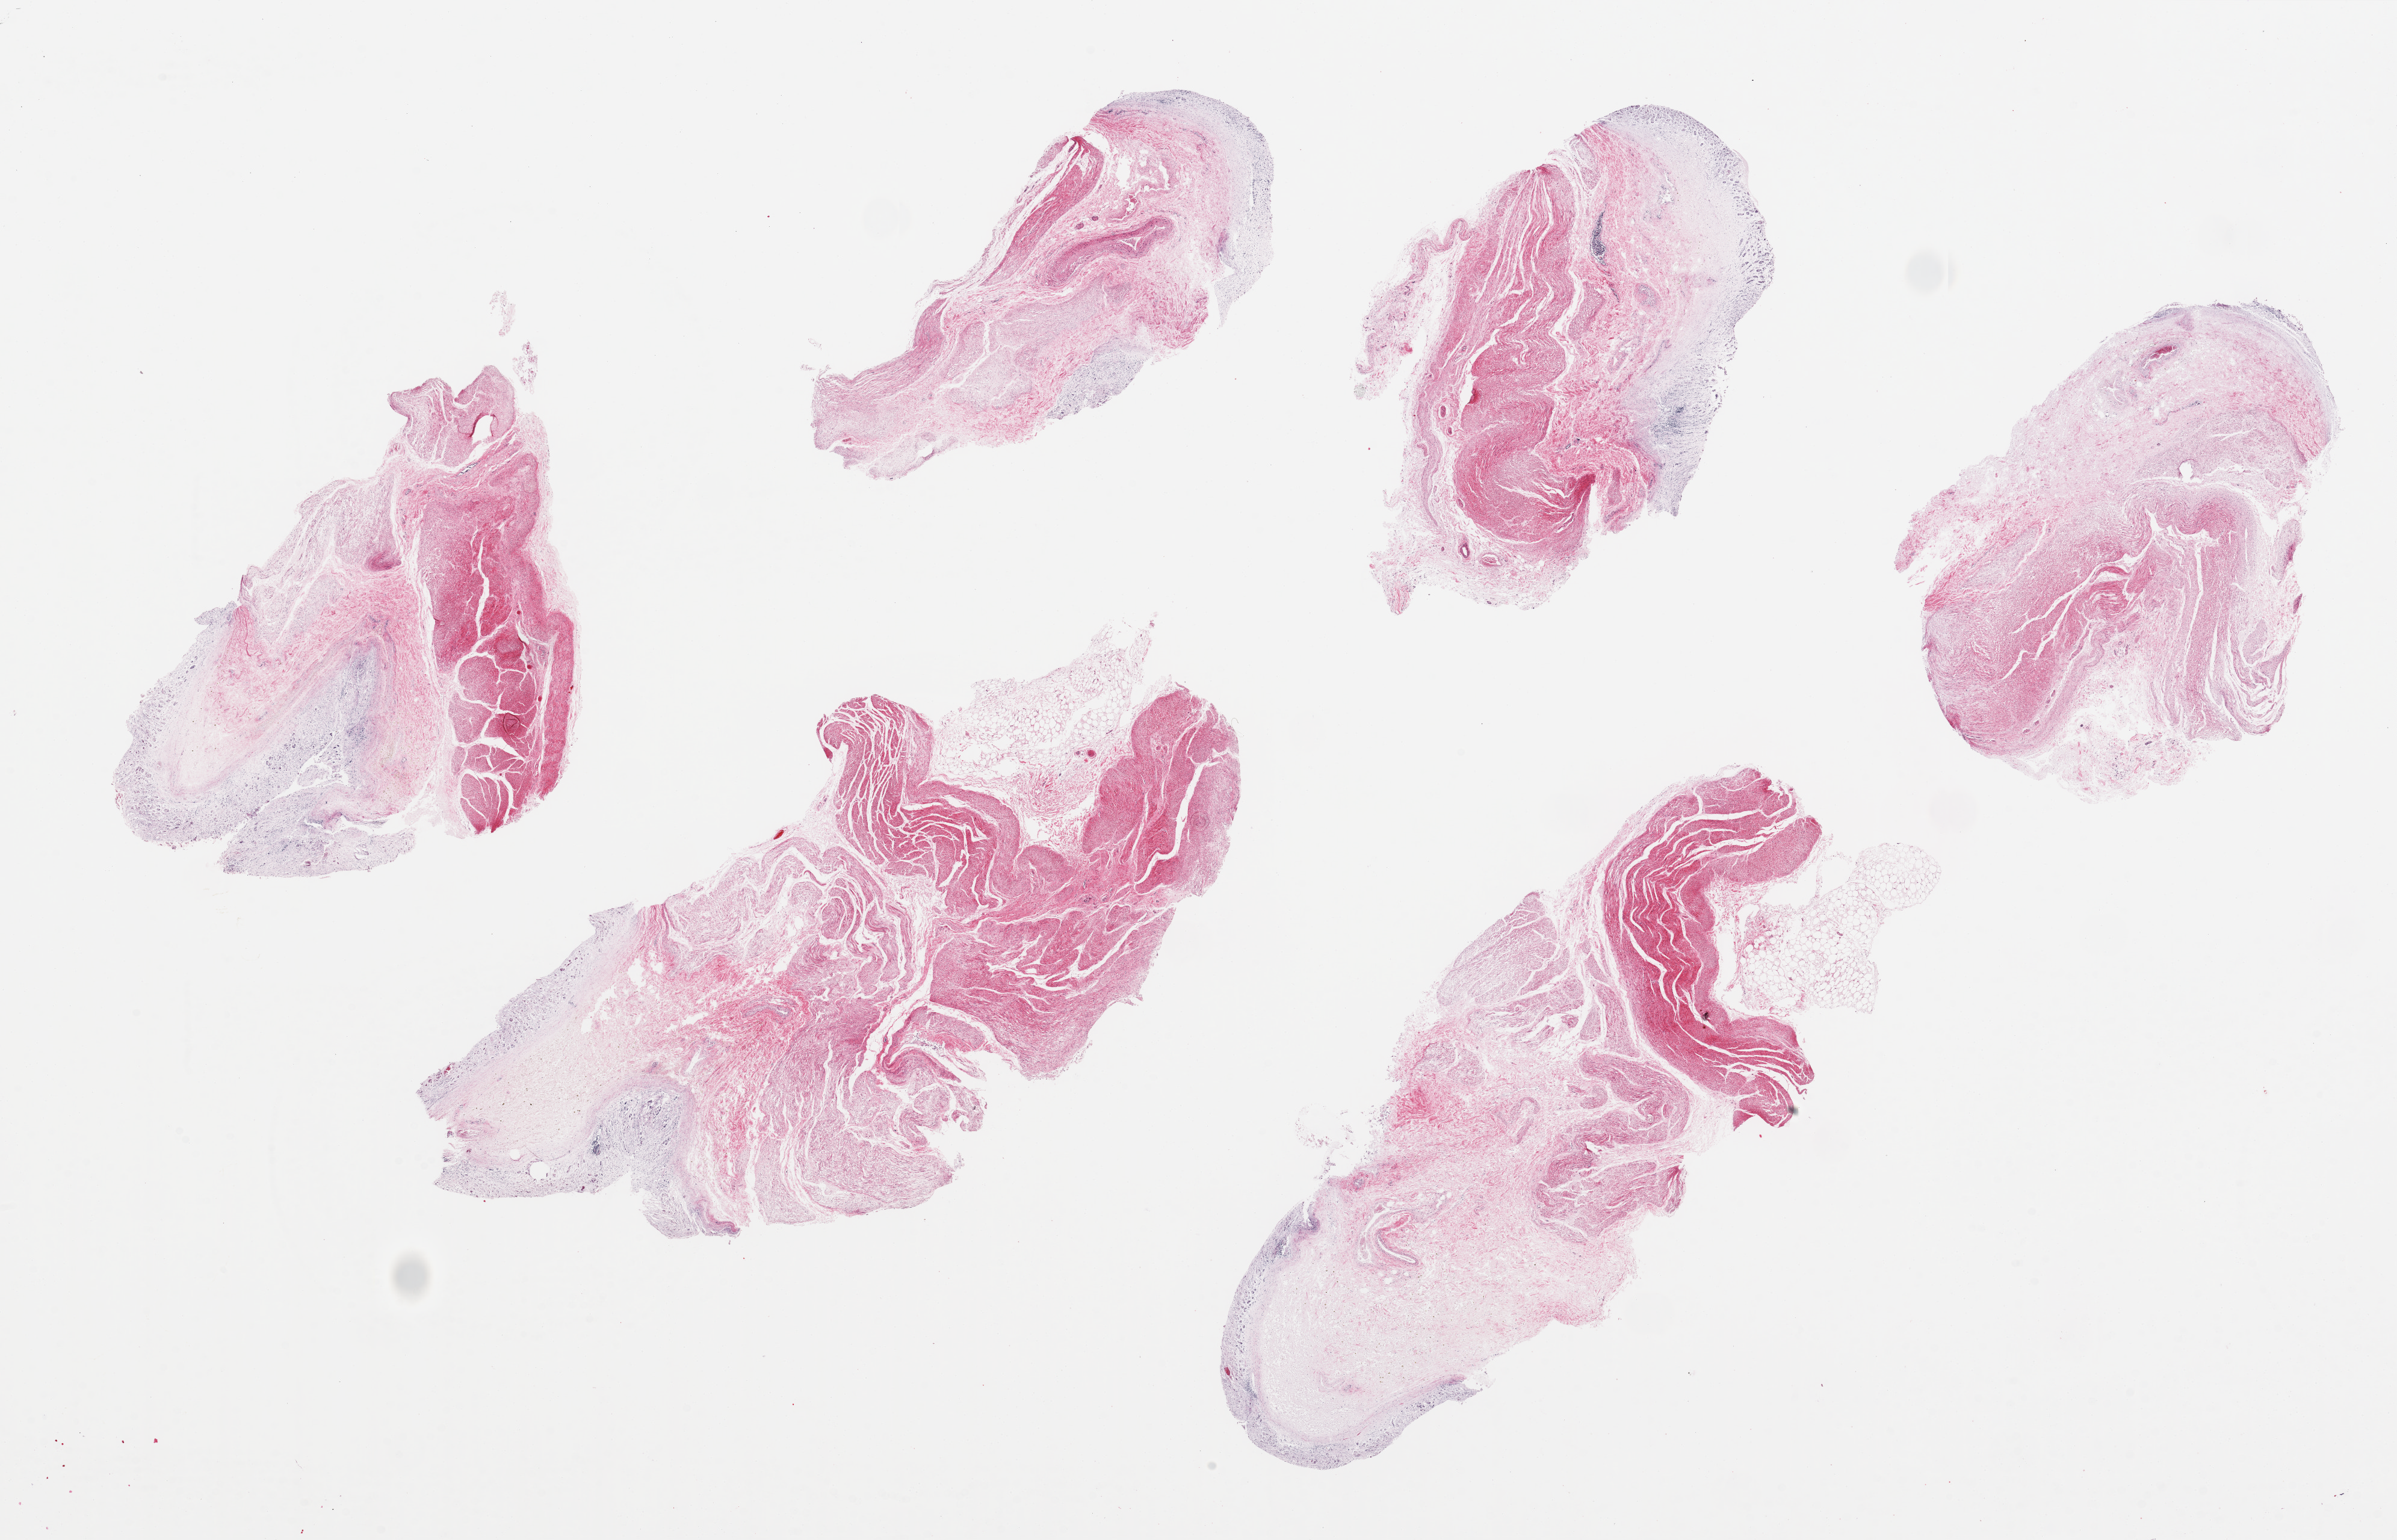
Digitized H&E-stained section — shown as a low-resolution overview of the whole scanned area (about 31.5 x 20.2 mm, from a 20x scan), PAXgene-fixed, paraffin-embedded tissue, sampled site (target tissue): stomach, tissue donor sample. Donor: male.
- review note (as recorded): 6 pieces, ~6x4mm. Mucosa completely autolyzed